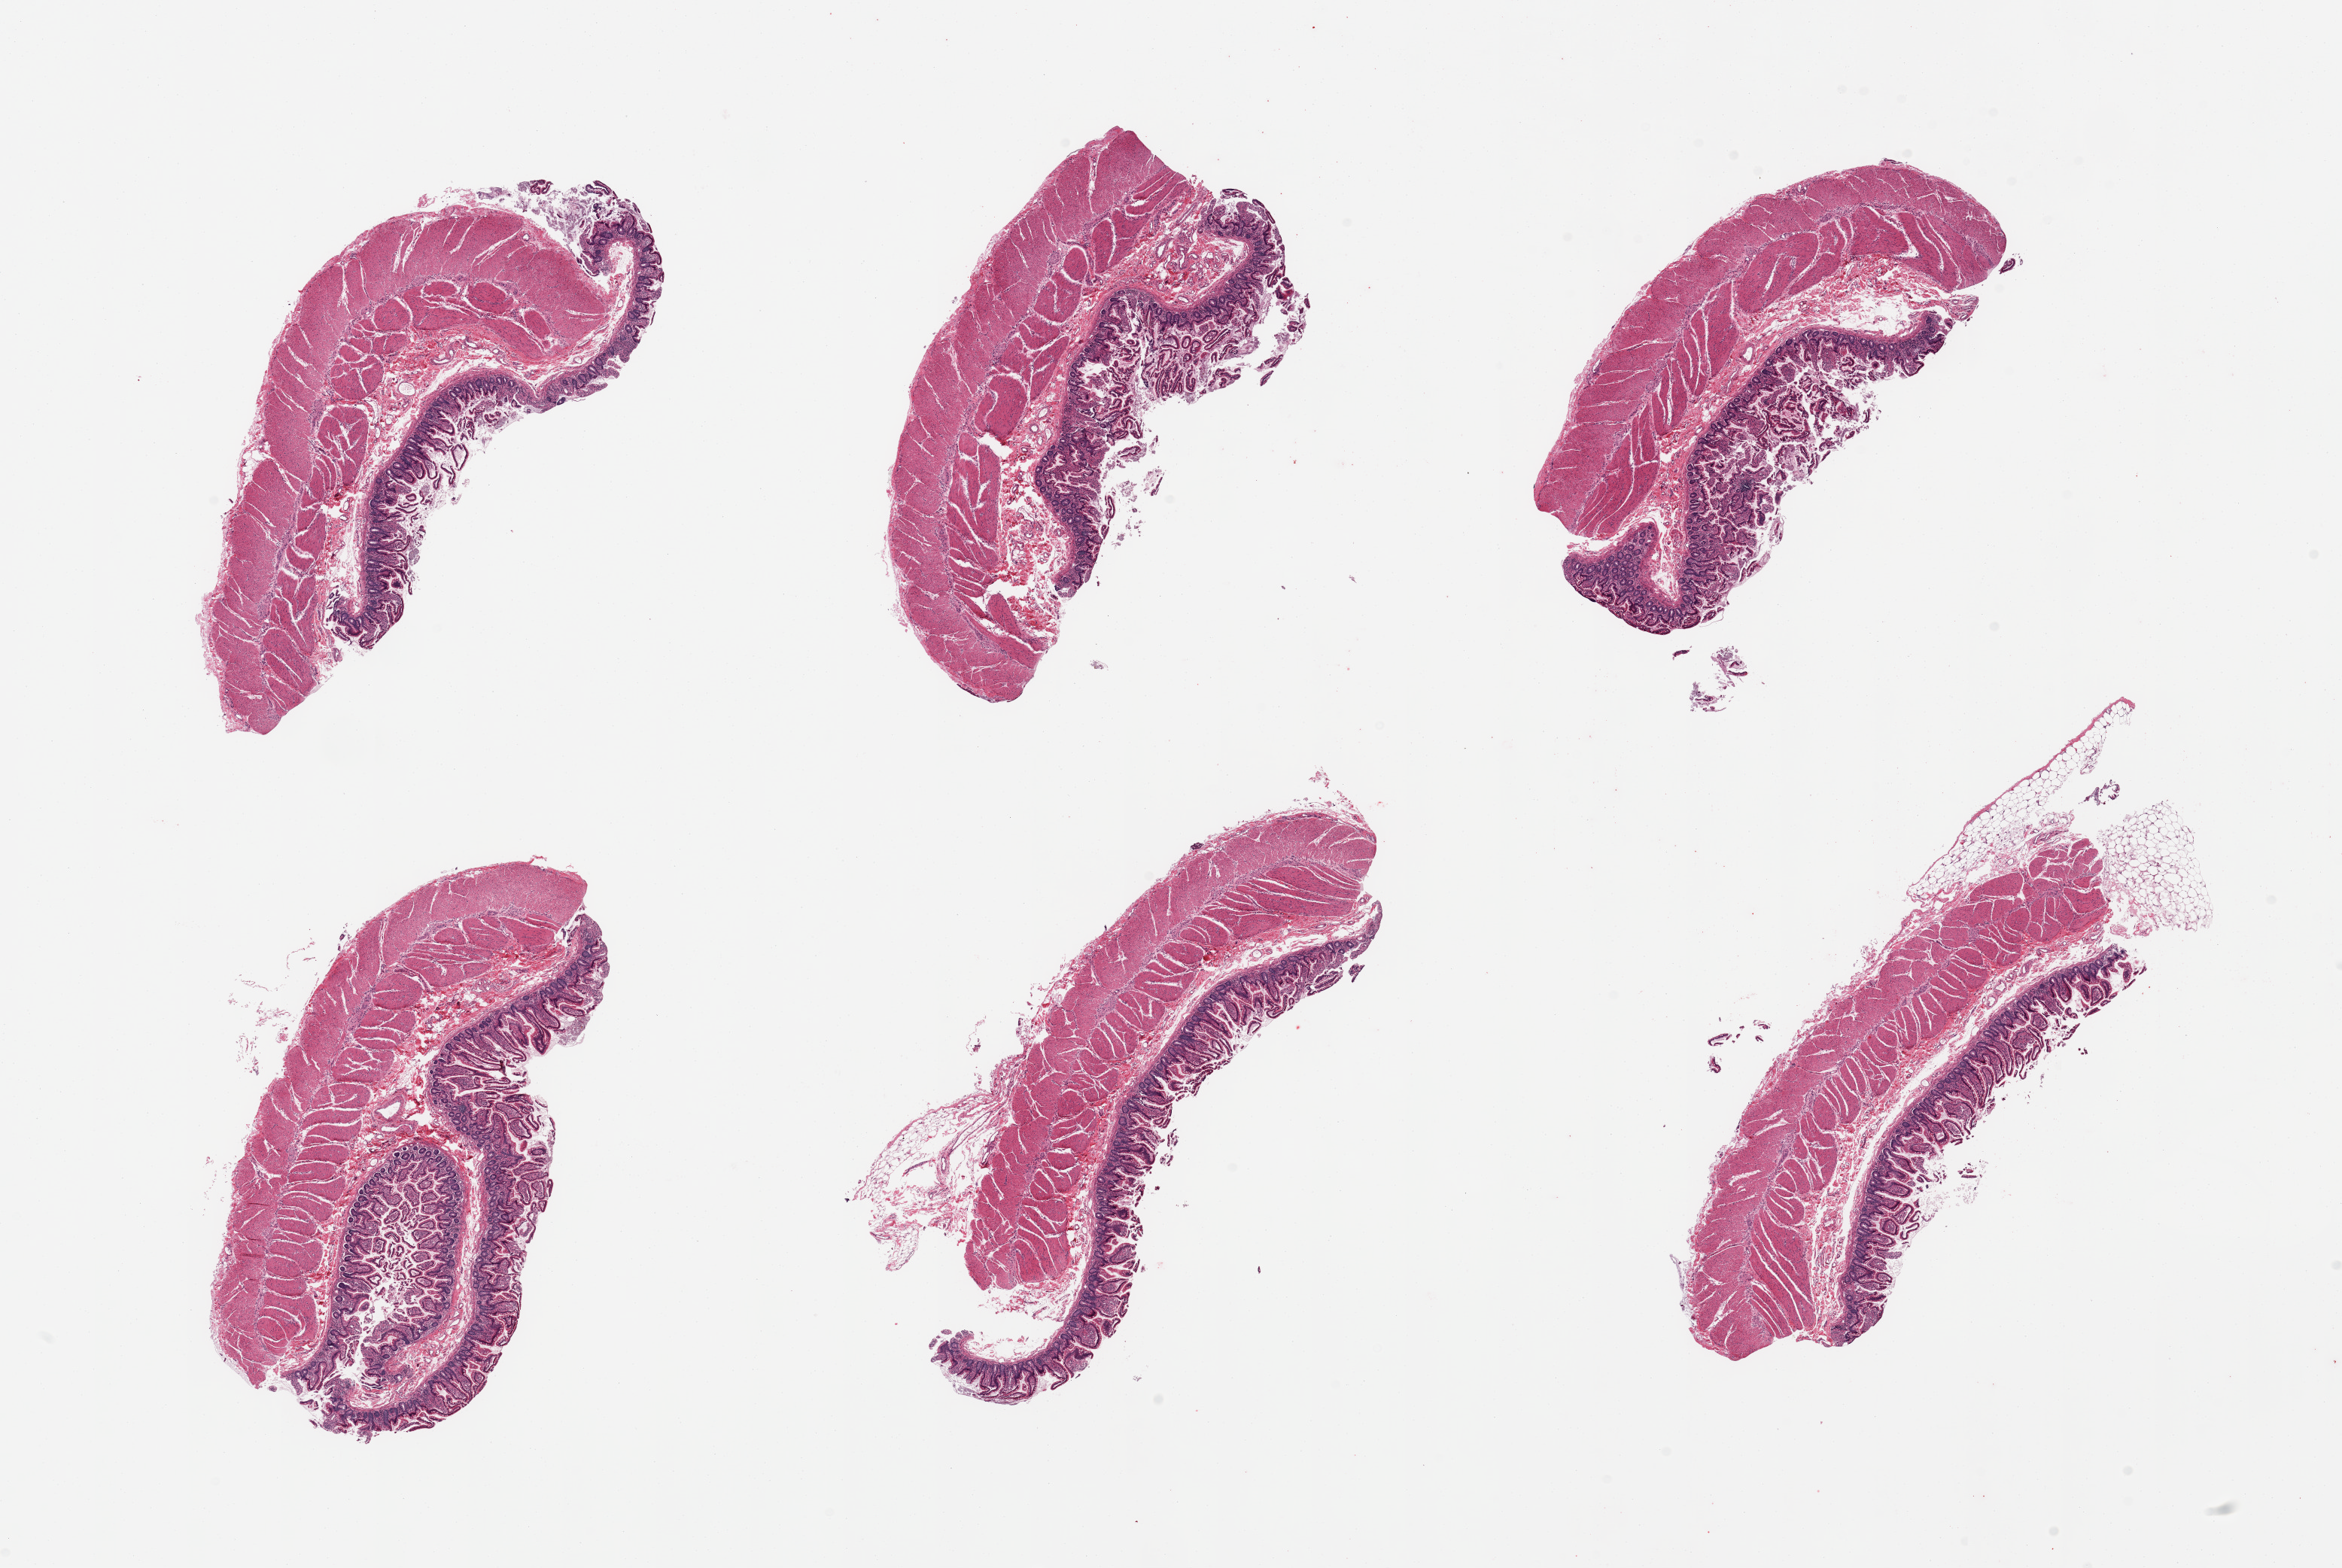
Whole-slide image, haematoxylin and eosin stain — whole scanned area (about 24.6 x 16.5 mm) shown as a low-resolution overview. Donor sex: male.
Specimen: PAXgene-fixed, paraffin-embedded tissue; sampled site (target tissue): transverse colon; donor tissue sample.